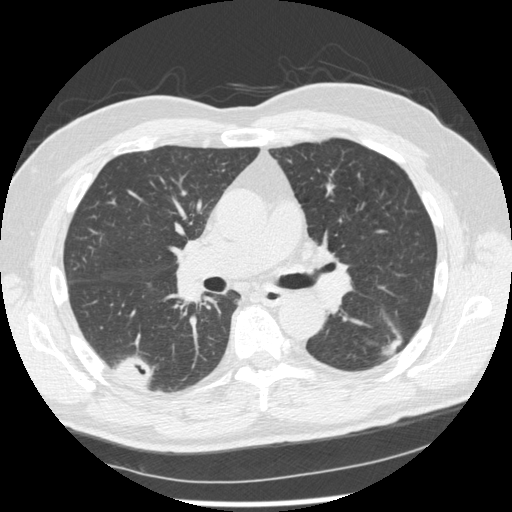
Low-dose screening chest CT, axial slice; second screening round (one year after baseline); lung window (W 1500 / L -600 HU); standard (soft-tissue) reconstruction kernel (STANDARD); 512 × 512 image matrix. Male participant, aged 74 years at enrolment. Former smoker at enrolment.
• Expert-annotated lung lesion, box from (x=372, y=317) to (x=420, y=369) px.
• The screening reader recorded 7 non-calcified nodules or masses ≥4 mm on this exam (right upper lobe, right lower lobe, right upper lobe, right lower lobe, left lower lobe, left upper lobe, left upper lobe); which of them this box marks is not recorded.
• Official screen result: positive, other.
• Later outcome: lung cancer diagnosed 43 days after this screen — squamous cell carcinoma, NOS, left lower lobe, well differentiated (G1), stage IA (AJCC 6th edition), 28 mm at pathology.